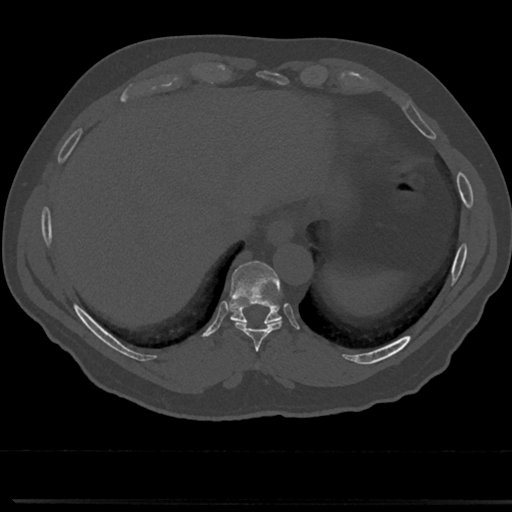
CT including the spine, one axial slice. Slice 284 of 817 in the series (ordered by position). 120 kVp. Bone window (W 1800 / L 400 HU). 512 × 512 image matrix, field of view 355 × 355 mm. Patient: male, 61 years. From the clinical record (not read from this slice): primary cancer: prostate.
Annotated regions visible in this slice (semi-automatic segmentation, software-assisted and operator-edited):
- T8 vertebra: bounding box <255,353,264,372> (left, top, right, bottom; pixels)
- T9 vertebra: <211,262,304,350>